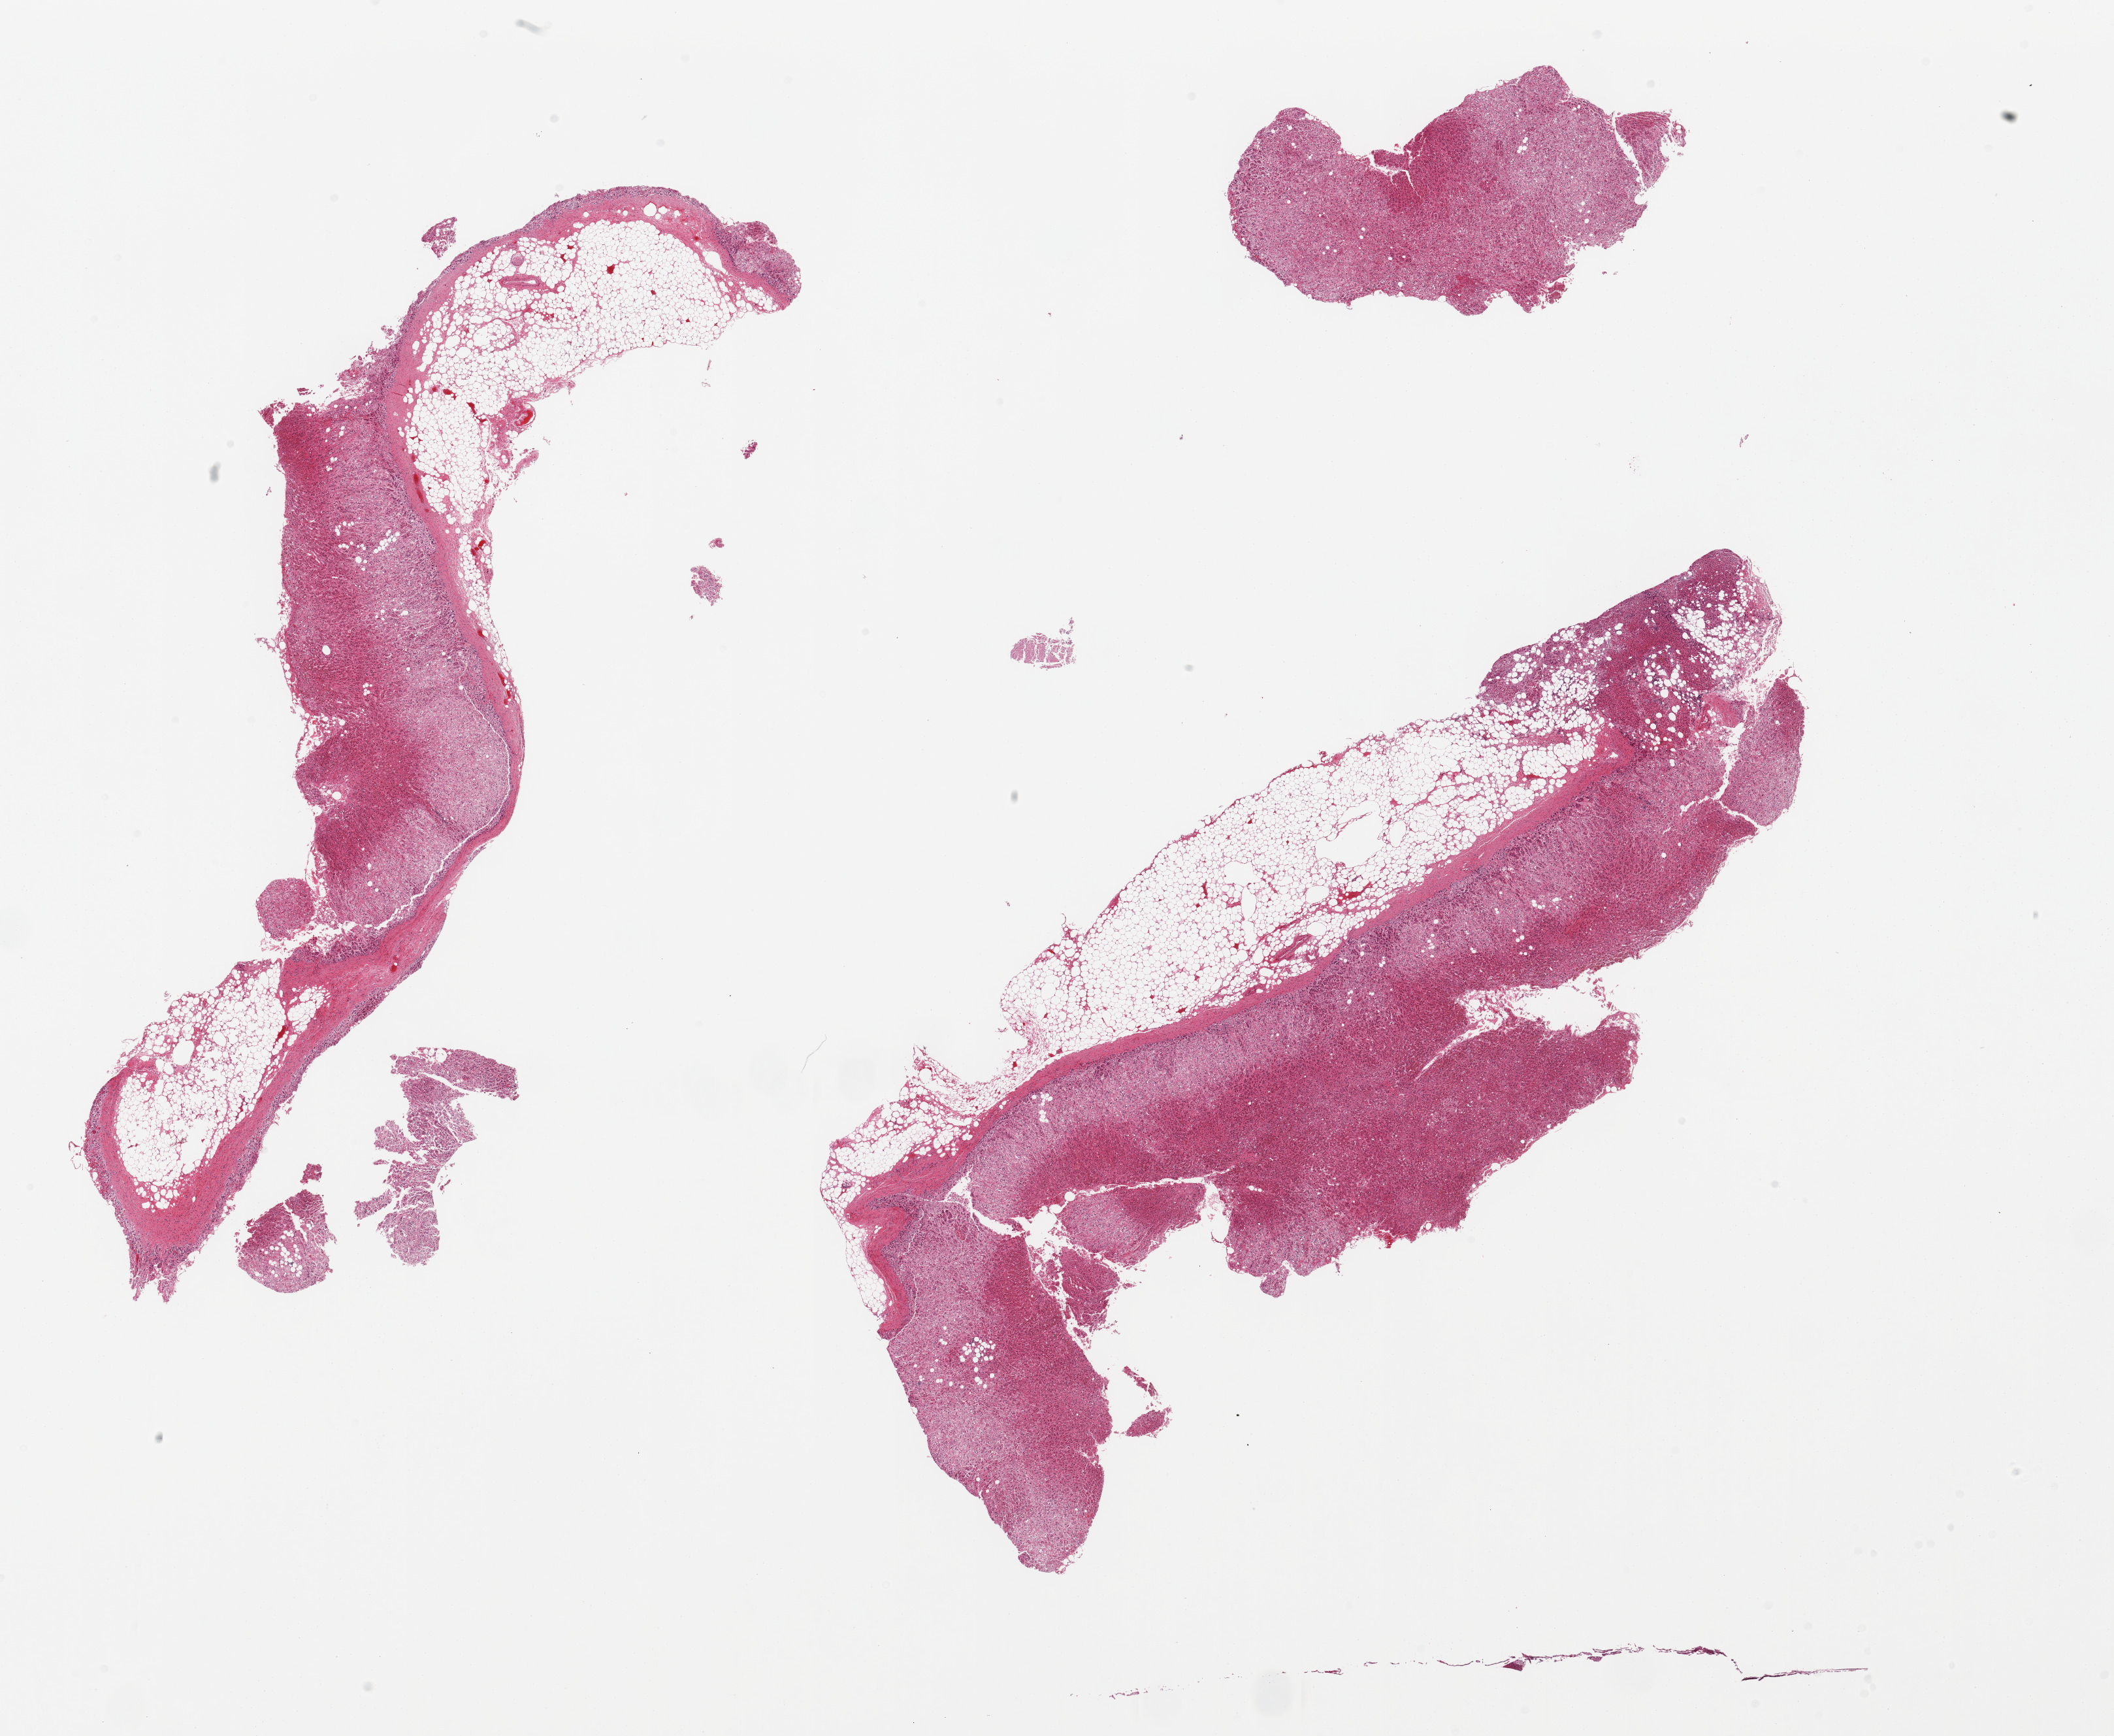
Haematoxylin and eosin whole-slide image, brightfield, whole scanned area (about 25.6 x 21.0 mm, from a 20x scan) shown as a low-resolution overview. PAXgene-fixed paraffin-embedded (PFPE) section. Section of adrenal gland (target tissue). Tissue donor sample. Donor sex: female.
Reviewer comment on this tissue sample: 3 pieces, fragmented; 30 and 50% attached fat.